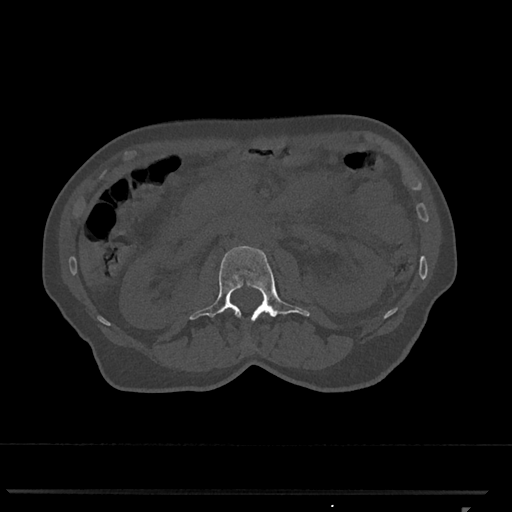
CT including the spine, one axial slice. Slice 347 of 793 in the series (ordered by position). Reconstruction kernel Br40s/3. Bone window (W 1800 / L 400 HU). 0.5 mm slice thickness. 512 × 512 image matrix. Female patient, age 62 years. From the clinical record (not read from this slice): primary cancer: renal.
Annotated regions visible in this slice (semi-automatically segmented with operator editing):
- L2 vertebra: bounding box [x1, y1, x2, y2] px = [189, 246, 310, 321]